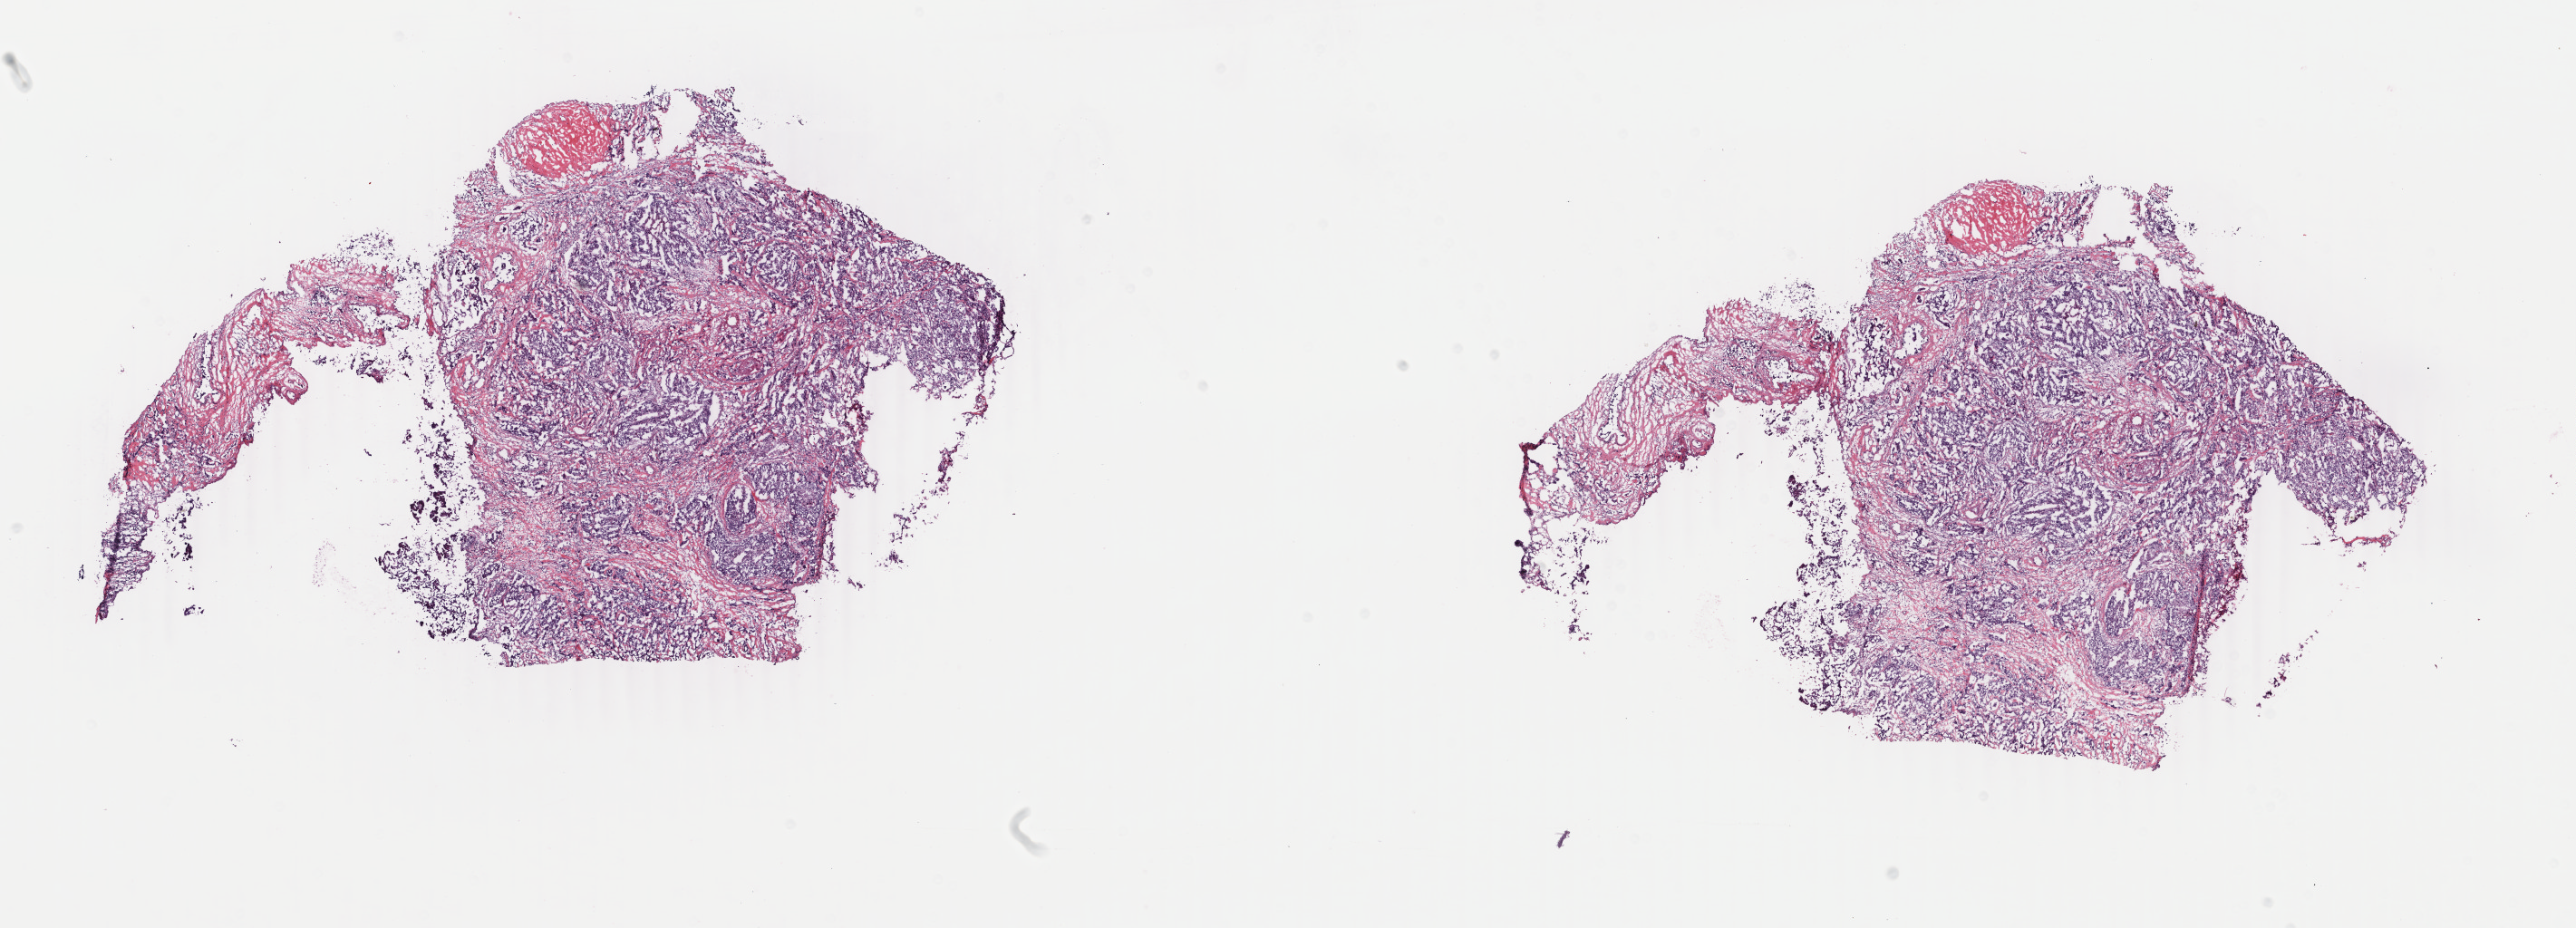
Digitized H&E-stained tissue section (whole slide), whole scanned area (about 22.6 x 8.1 mm) shown as a low-resolution overview. Frozen section. Sample: primary tumour, breast. Female, age 61 years at initial diagnosis. Pathologist review of this section (percent, as recorded): tumour cells 80%, tumour nuclei 80%, normal cells 0%, stromal cells 20%, necrosis 0%. Infiltration values recorded for this section: lymphocyte infiltration 0%, monocyte infiltration 0%, neutrophil infiltration 0%.
Laterality: right. Histologic diagnosis: Infiltrating duct carcinoma, NOS.